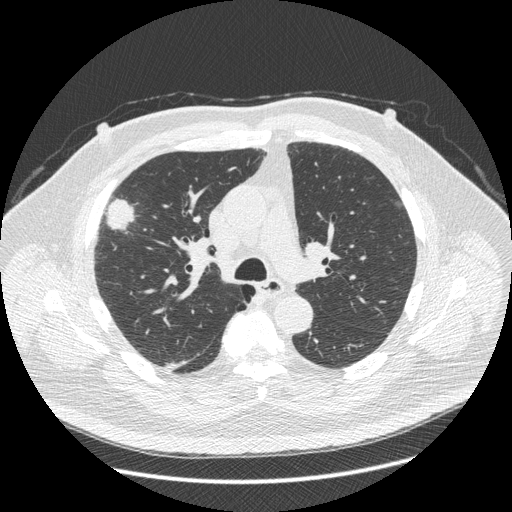
Low-dose screening chest CT, one axial slice; position 277 of 426 along the scan axis; reconstruction kernel STANDARD; 120 kVp; lung window (W 1500 / L -600 HU); 1.25 mm slice thickness; 512 × 512 image matrix, field of view 400 × 400 mm.
Structures marked on this image (manually delineated by an expert):
- lesion 1 (tumor, upper lobe of right lung): bounding box [x1, y1, x2, y2] px = [107, 199, 134, 230]